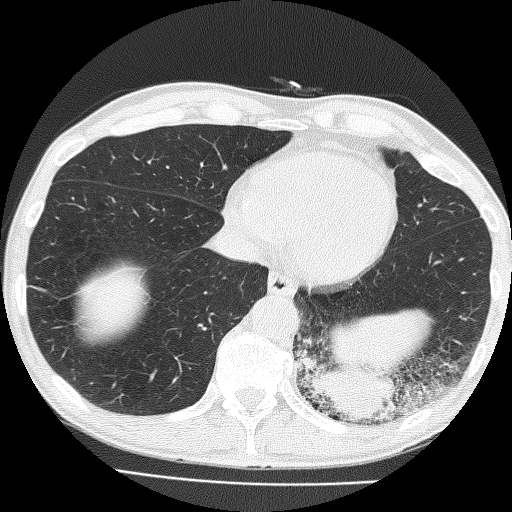
Low-dose screening chest CT, axial slice; first (baseline) screen; lung window (W 1500 / L -600 HU); lung (sharp) reconstruction kernel (FC51); 120 kVp; slice 111 of 160 in the series. Male participant, aged 58 years at enrolment. Current smoker at enrolment.
• Expert-annotated lung lesion, box from (x=289, y=292) to (x=431, y=435) px.
• The screening reader recorded 2 non-calcified nodules or masses ≥4 mm on this exam (left lower lobe, left upper lobe); which of them this box marks is not recorded.
• Lung cancer was diagnosed 39 days after this screen: non-small cell carcinoma, left lower lobe, poorly differentiated (G3), stage IV (AJCC 6th edition), 74 mm at pathology.